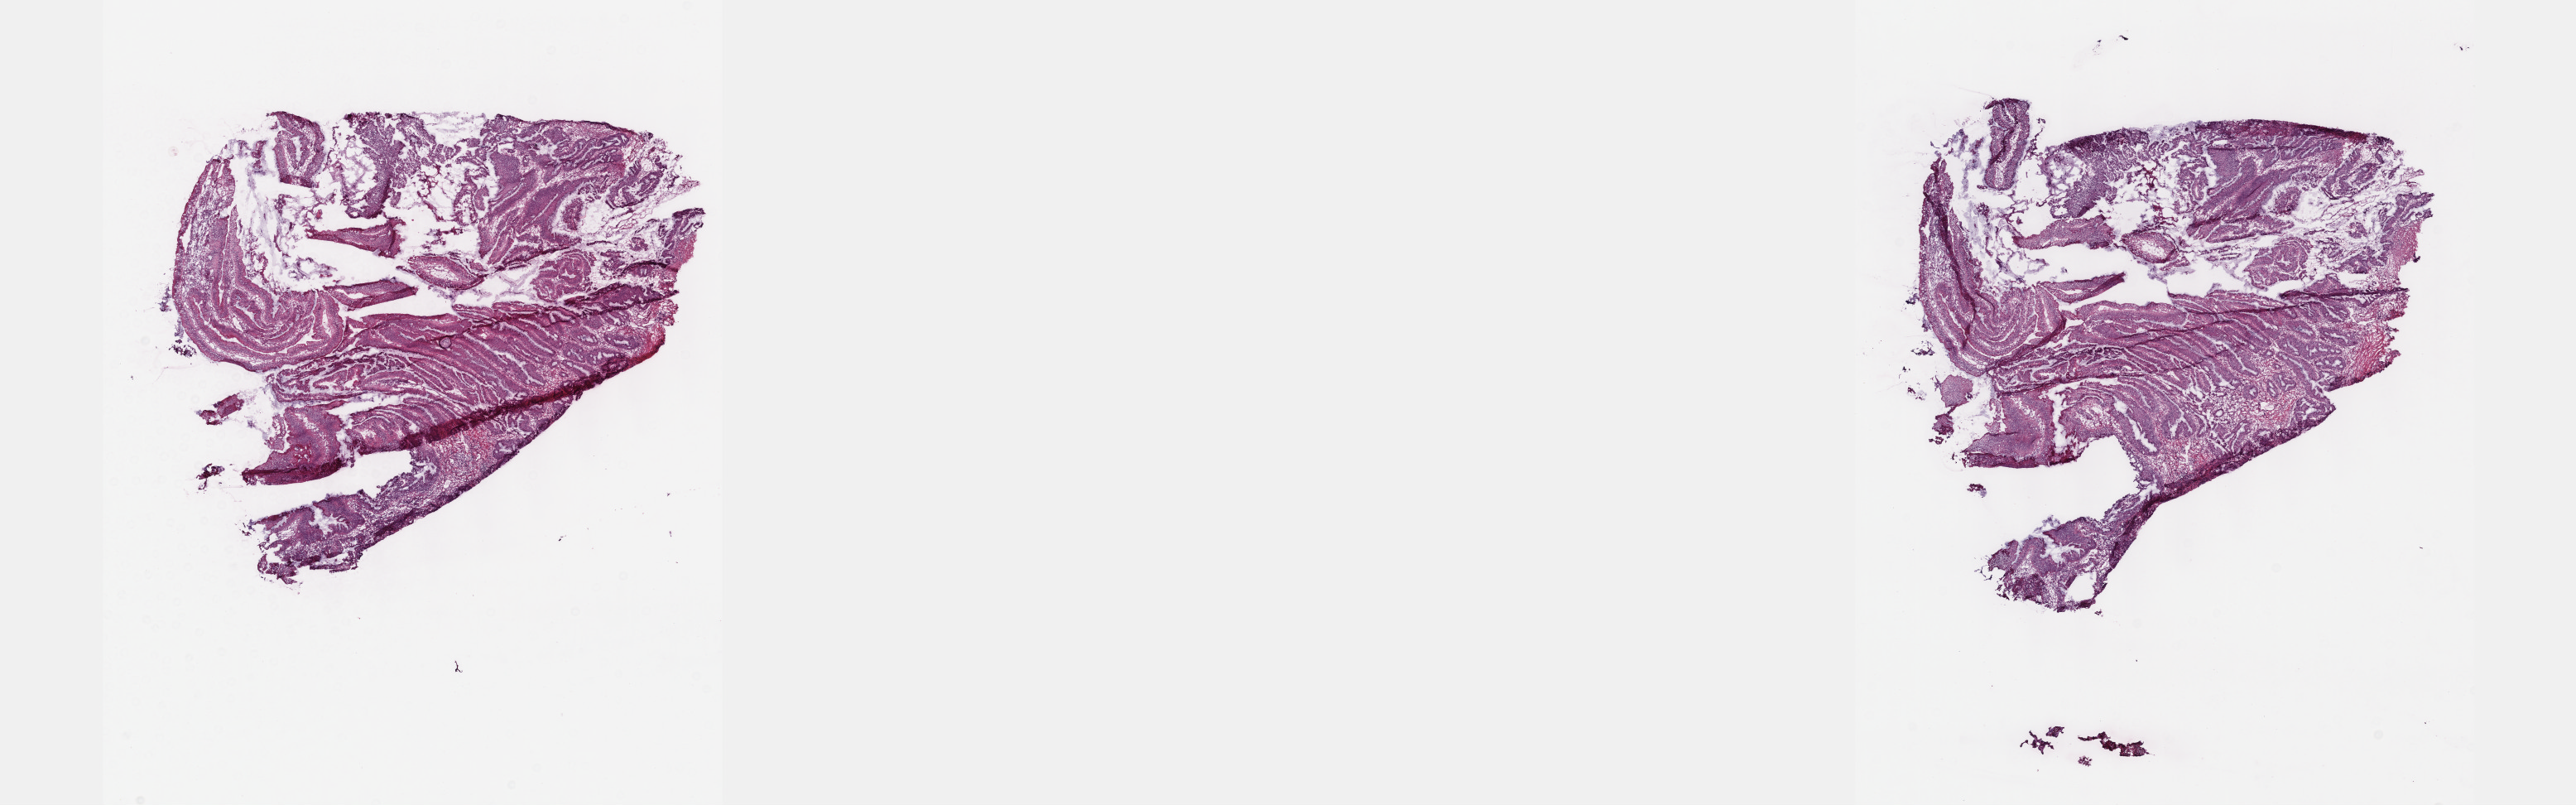
Whole-slide histology image, H&E-stained — whole scanned area (about 25.1 x 7.9 mm) shown as a low-resolution overview, frozen section from the bottom of the tissue portion, colon, primary tumour sample. Patient: male, age at initial diagnosis 81 years. Composition of this section per pathologist review: tumour cells 88%, tumour nuclei 70%, normal cells 0%, stromal cells 10%, necrosis 2%. Inflammatory infiltration, as recorded: lymphocyte infiltration 15%, monocyte infiltration 3%, neutrophil infiltration 1%.
* lymph nodes positive (case pathology): 0 of 14 examined
* AJCC pathologic stage: II (5th edition)
* diagnosis: Adenocarcinoma, NOS